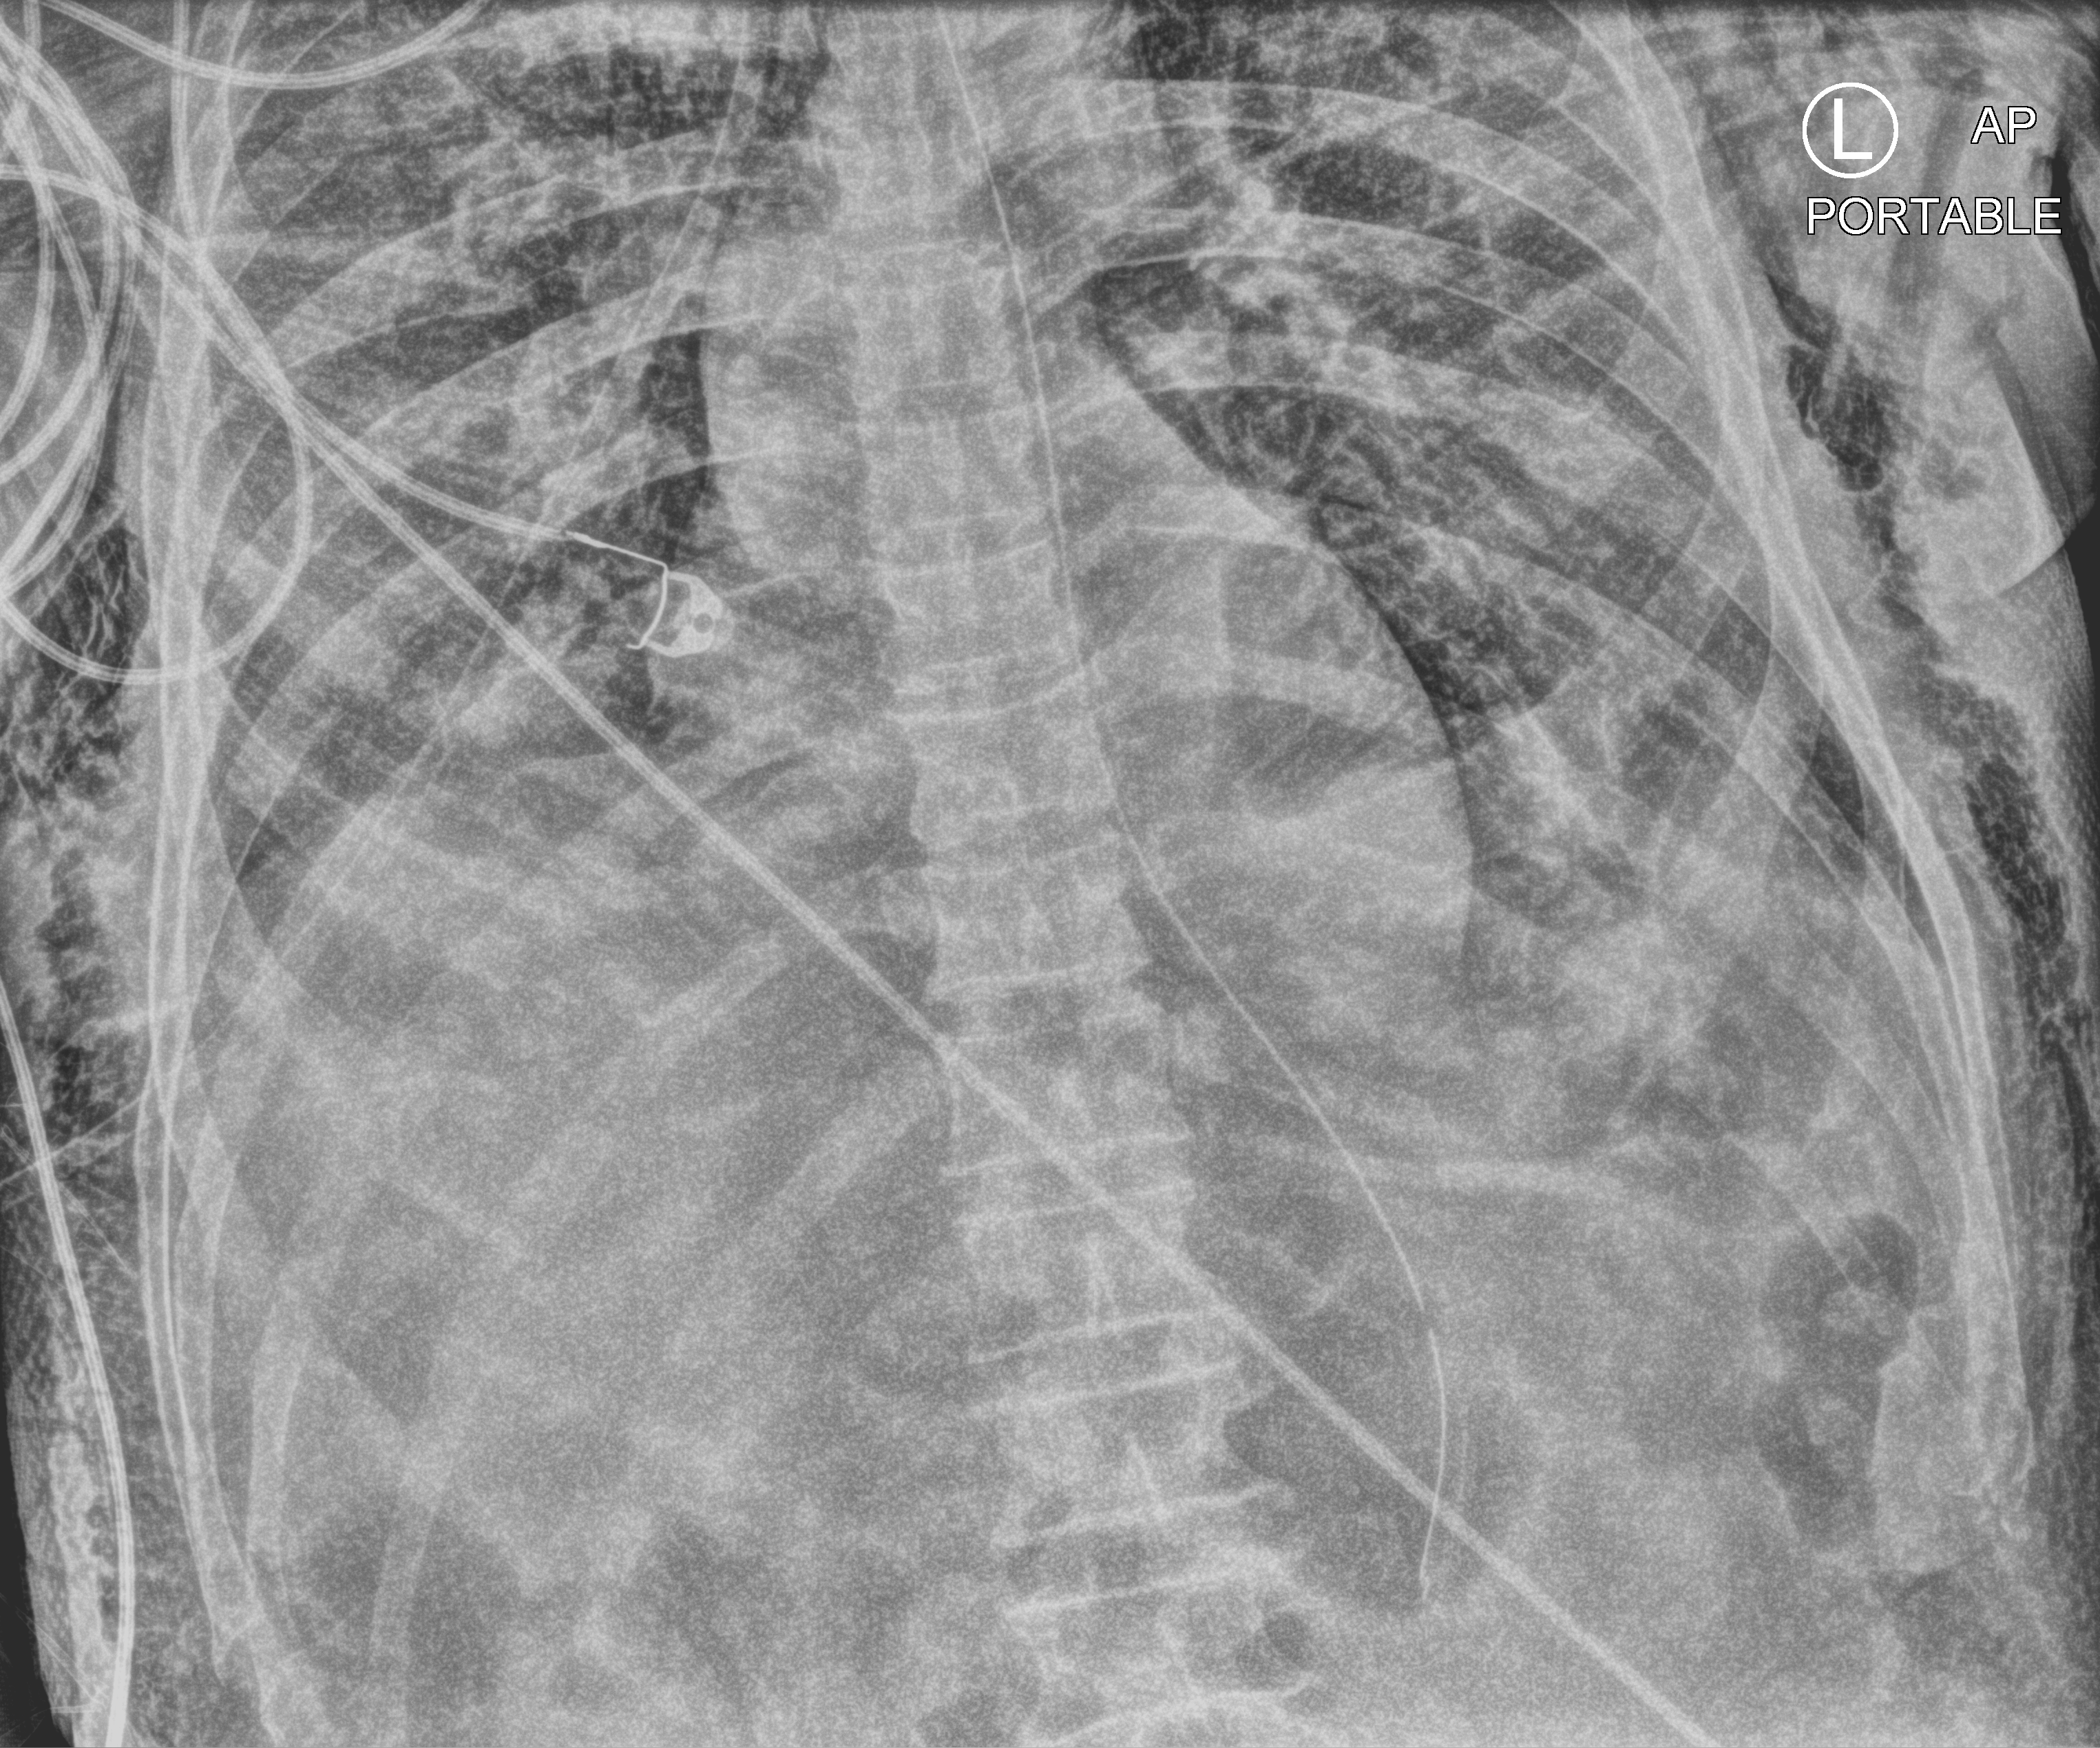
Chest X-ray (portable); anteroposterior (AP) projection. Patient hospitalised with COVID-19; male, aged 60–74 years.
From the hospital-stay record, not from the radiograph (when in the stay this image was taken is not recorded):
- COPD (admission record): no
- mechanically ventilated during this hospital stay: yes